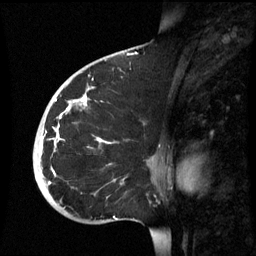
Breast MRI (dynamic contrast-enhanced), one sagittal slice; dynamic contrast-enhanced series, image 2 of 3 at this slice position (ordered by acquisition); 1.5 T; TE 4.2 ms, TR 8.9 ms; 2.6 mm slice thickness; 256 × 256 image matrix. Female patient, age 35 years. Case-level facts recorded for this patient, not image findings: setting: breast cancer imaged before/during neoadjuvant chemotherapy; receptor status: HR-positive, HER2-negative.
Outlined on this slice (semi-automatically segmented with operator editing):
- analysis volume of interest (the breast-tissue region the enhancement analysis was run in; not a lesion): bounding box [x1, y1, x2, y2] px = [33, 74, 163, 221]
- tumour enhancement mask (voxels above the 70 % enhancement threshold inside the analysis volume of interest): [49, 88, 107, 185]